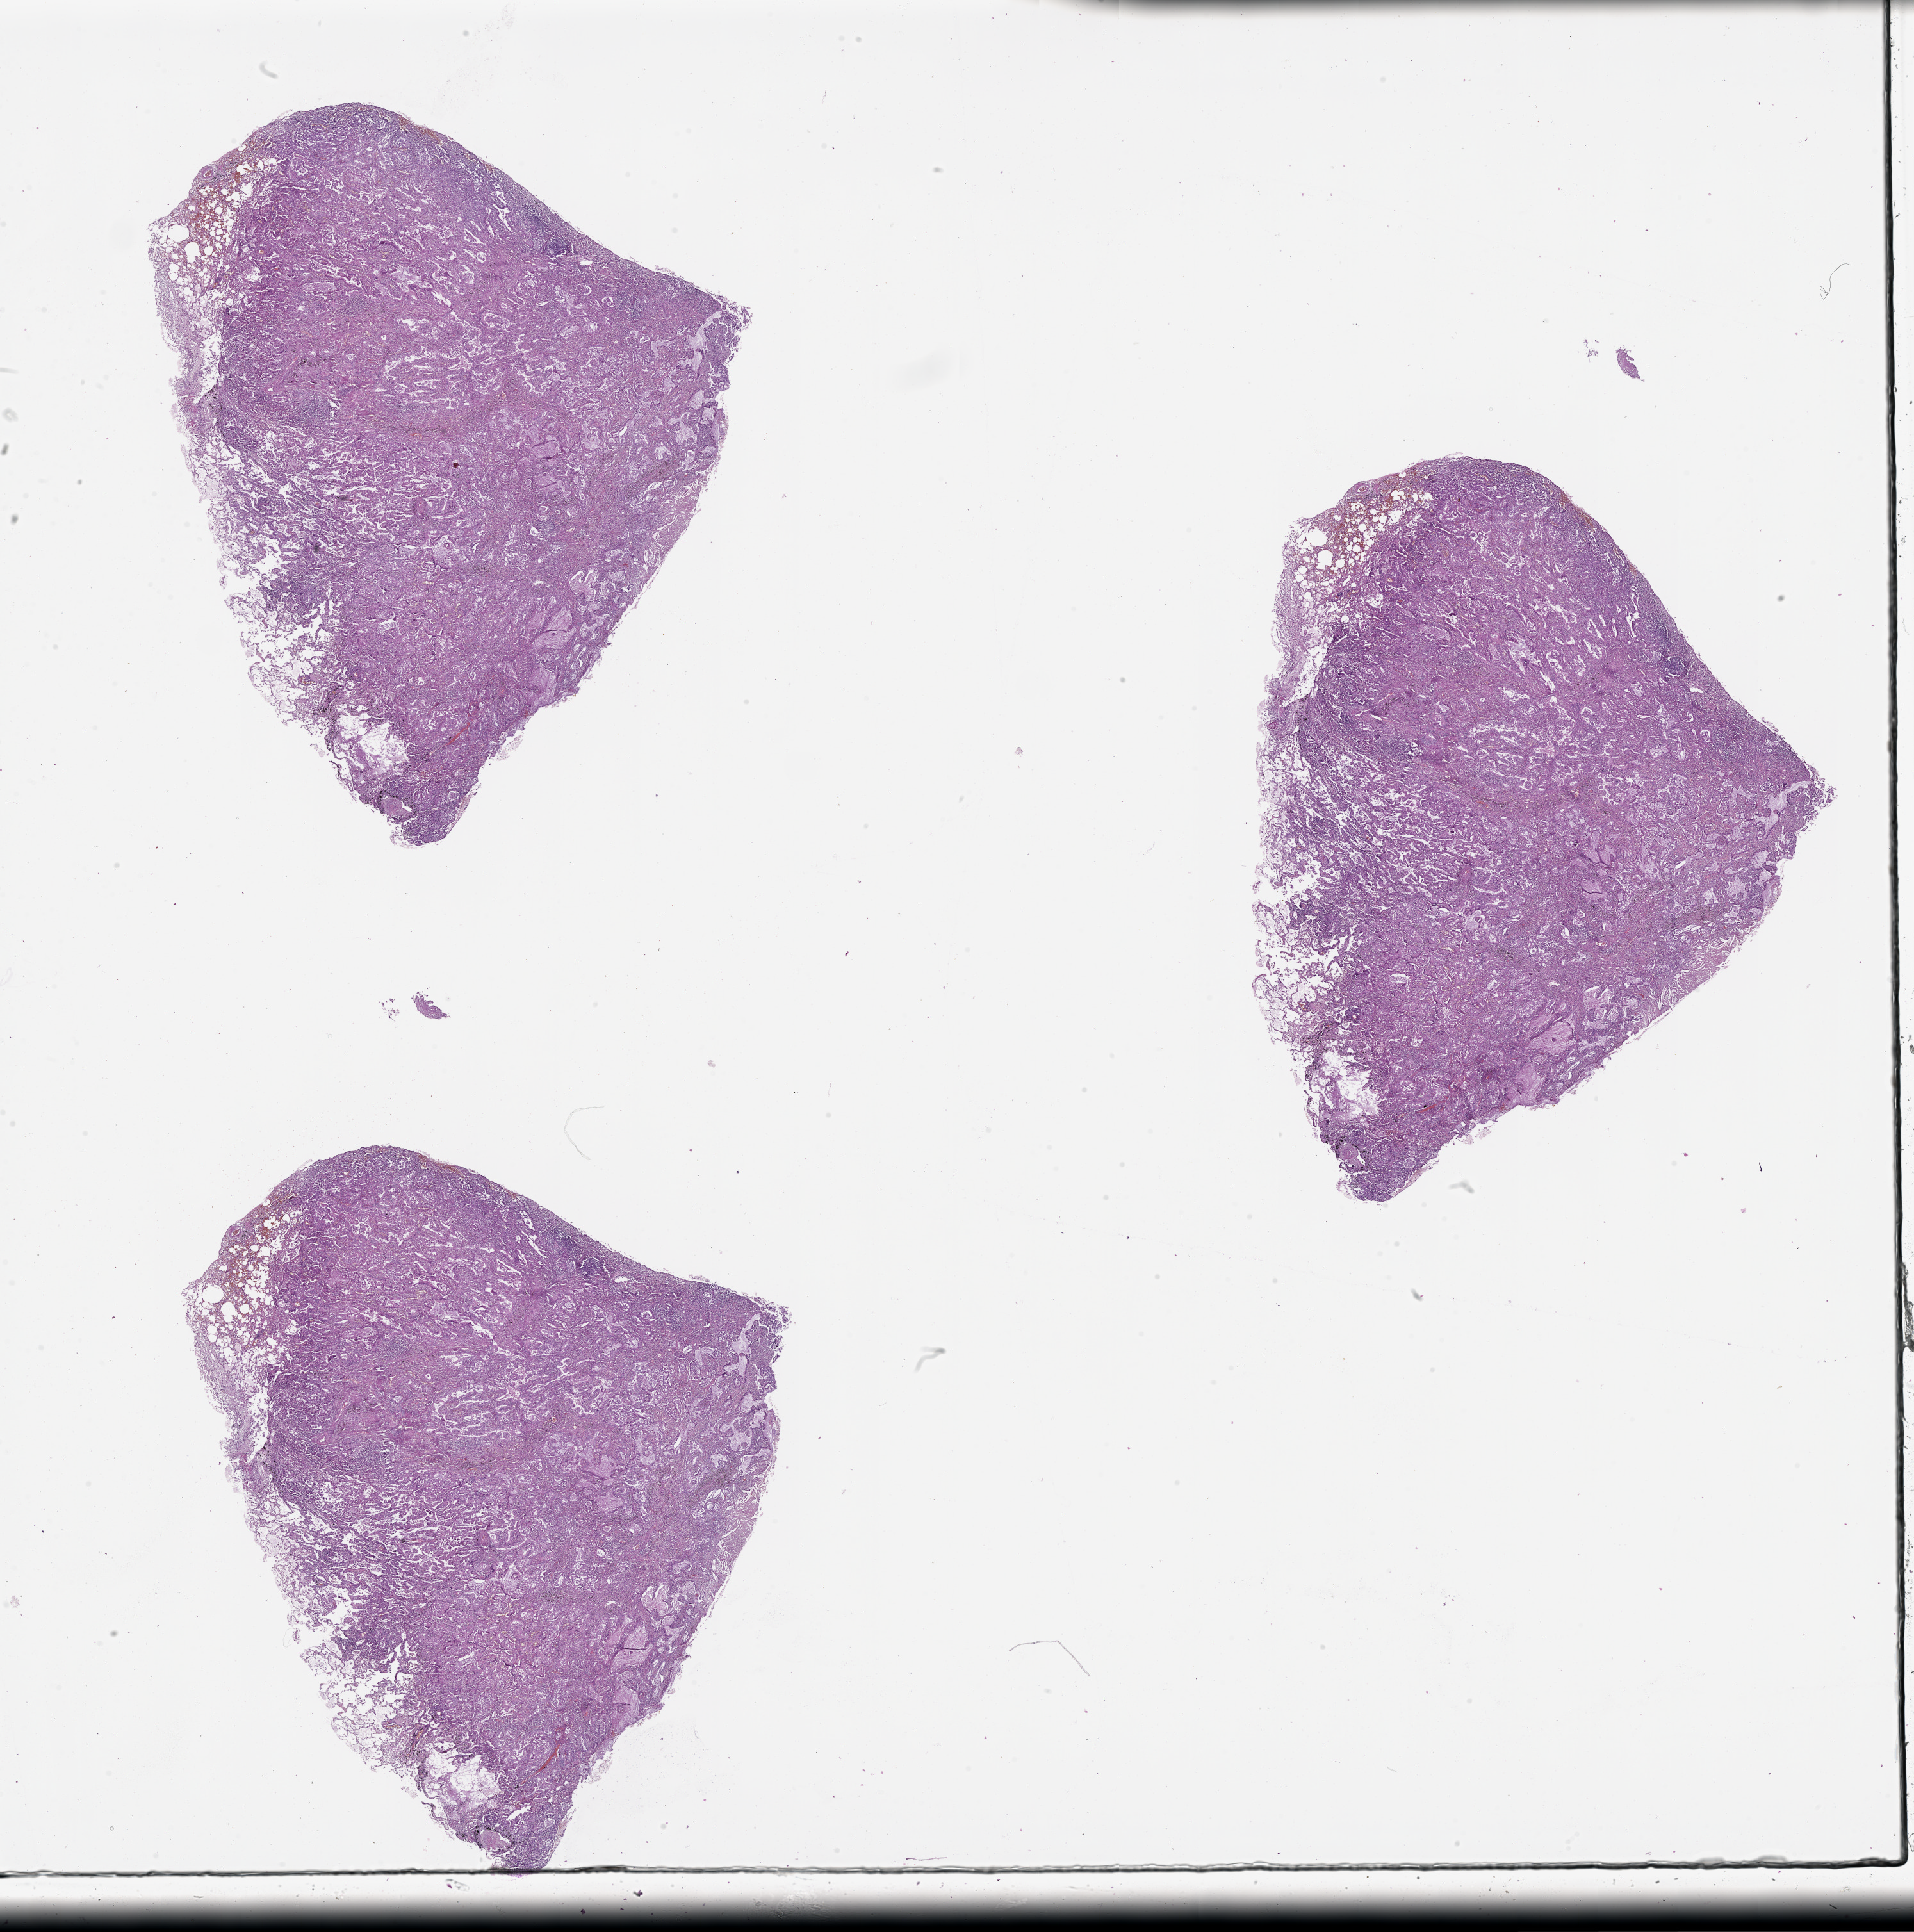
Digitized Hematoxylin and eosin (H&E) stained tissue section (whole slide) — a low-resolution overview of the entire scanned area, about 24.1 x 24.3 mm (acquisition: 20x scan); lung, tissue type not recorded.
Patient diagnosis (cohort enrolment): lung adenocarcinoma (lung).